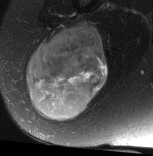
MRI of an extremity soft-tissue mass, one axial slice; position 32 of 77 along the scan axis; T2-weighted fat-saturated; MR volume resampled by the dataset authors to the PET/CT grid (not the native acquisition matrix); 3.27 mm slice thickness; 153 × 156 image matrix. Female patient. Case-level facts recorded for this patient, not image findings: histological type: synovial sarcoma; grade: intermediate; site of the primary tumour: right buttock.
Annotated regions visible in this slice (expert contour drawn on MRI and transferred to this co-registered scan by the dataset authors):
- gross tumour volume including surrounding oedema: bounding box <26,24,107,121> (left, top, right, bottom; pixels)
- gross tumour volume (mass): <26,24,107,121>